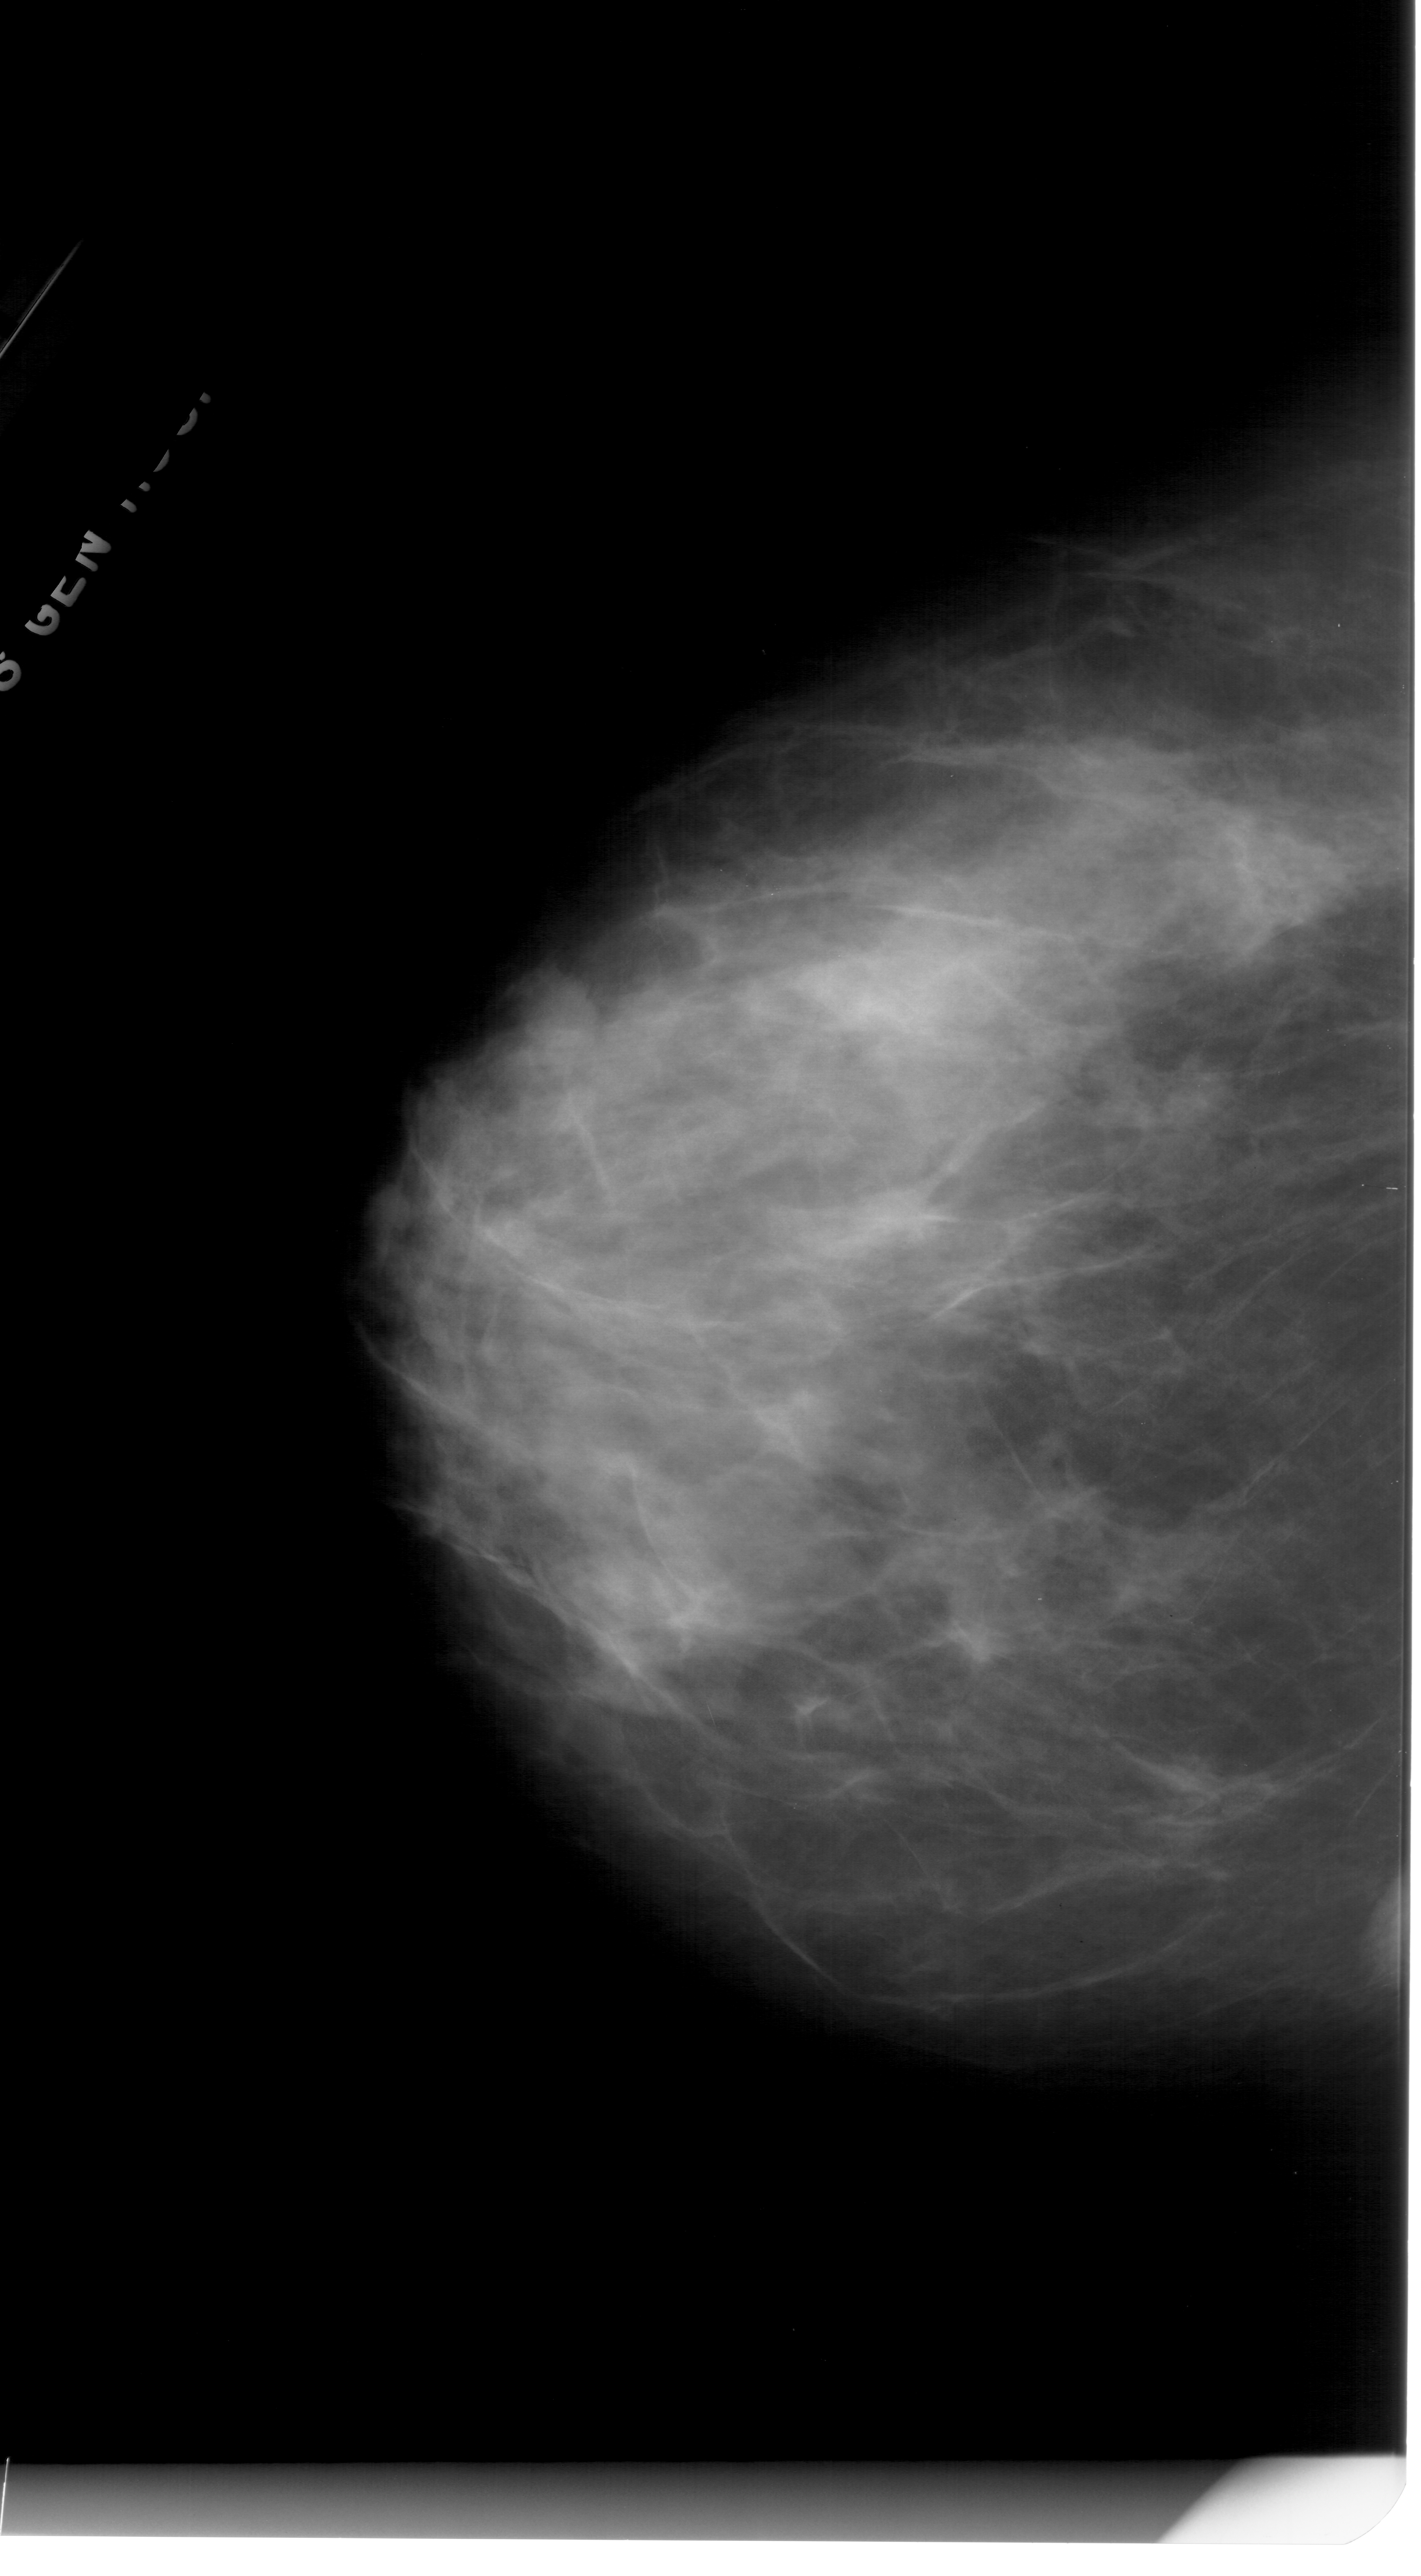
Digitized screen-film mammogram; left breast; CC view; BI-RADS breast density category 4 (scale 1–4).
Mass, shape oval, margins ill defined; BI-RADS assessment category 4; pathology result (as recorded, not read from the image): benign.